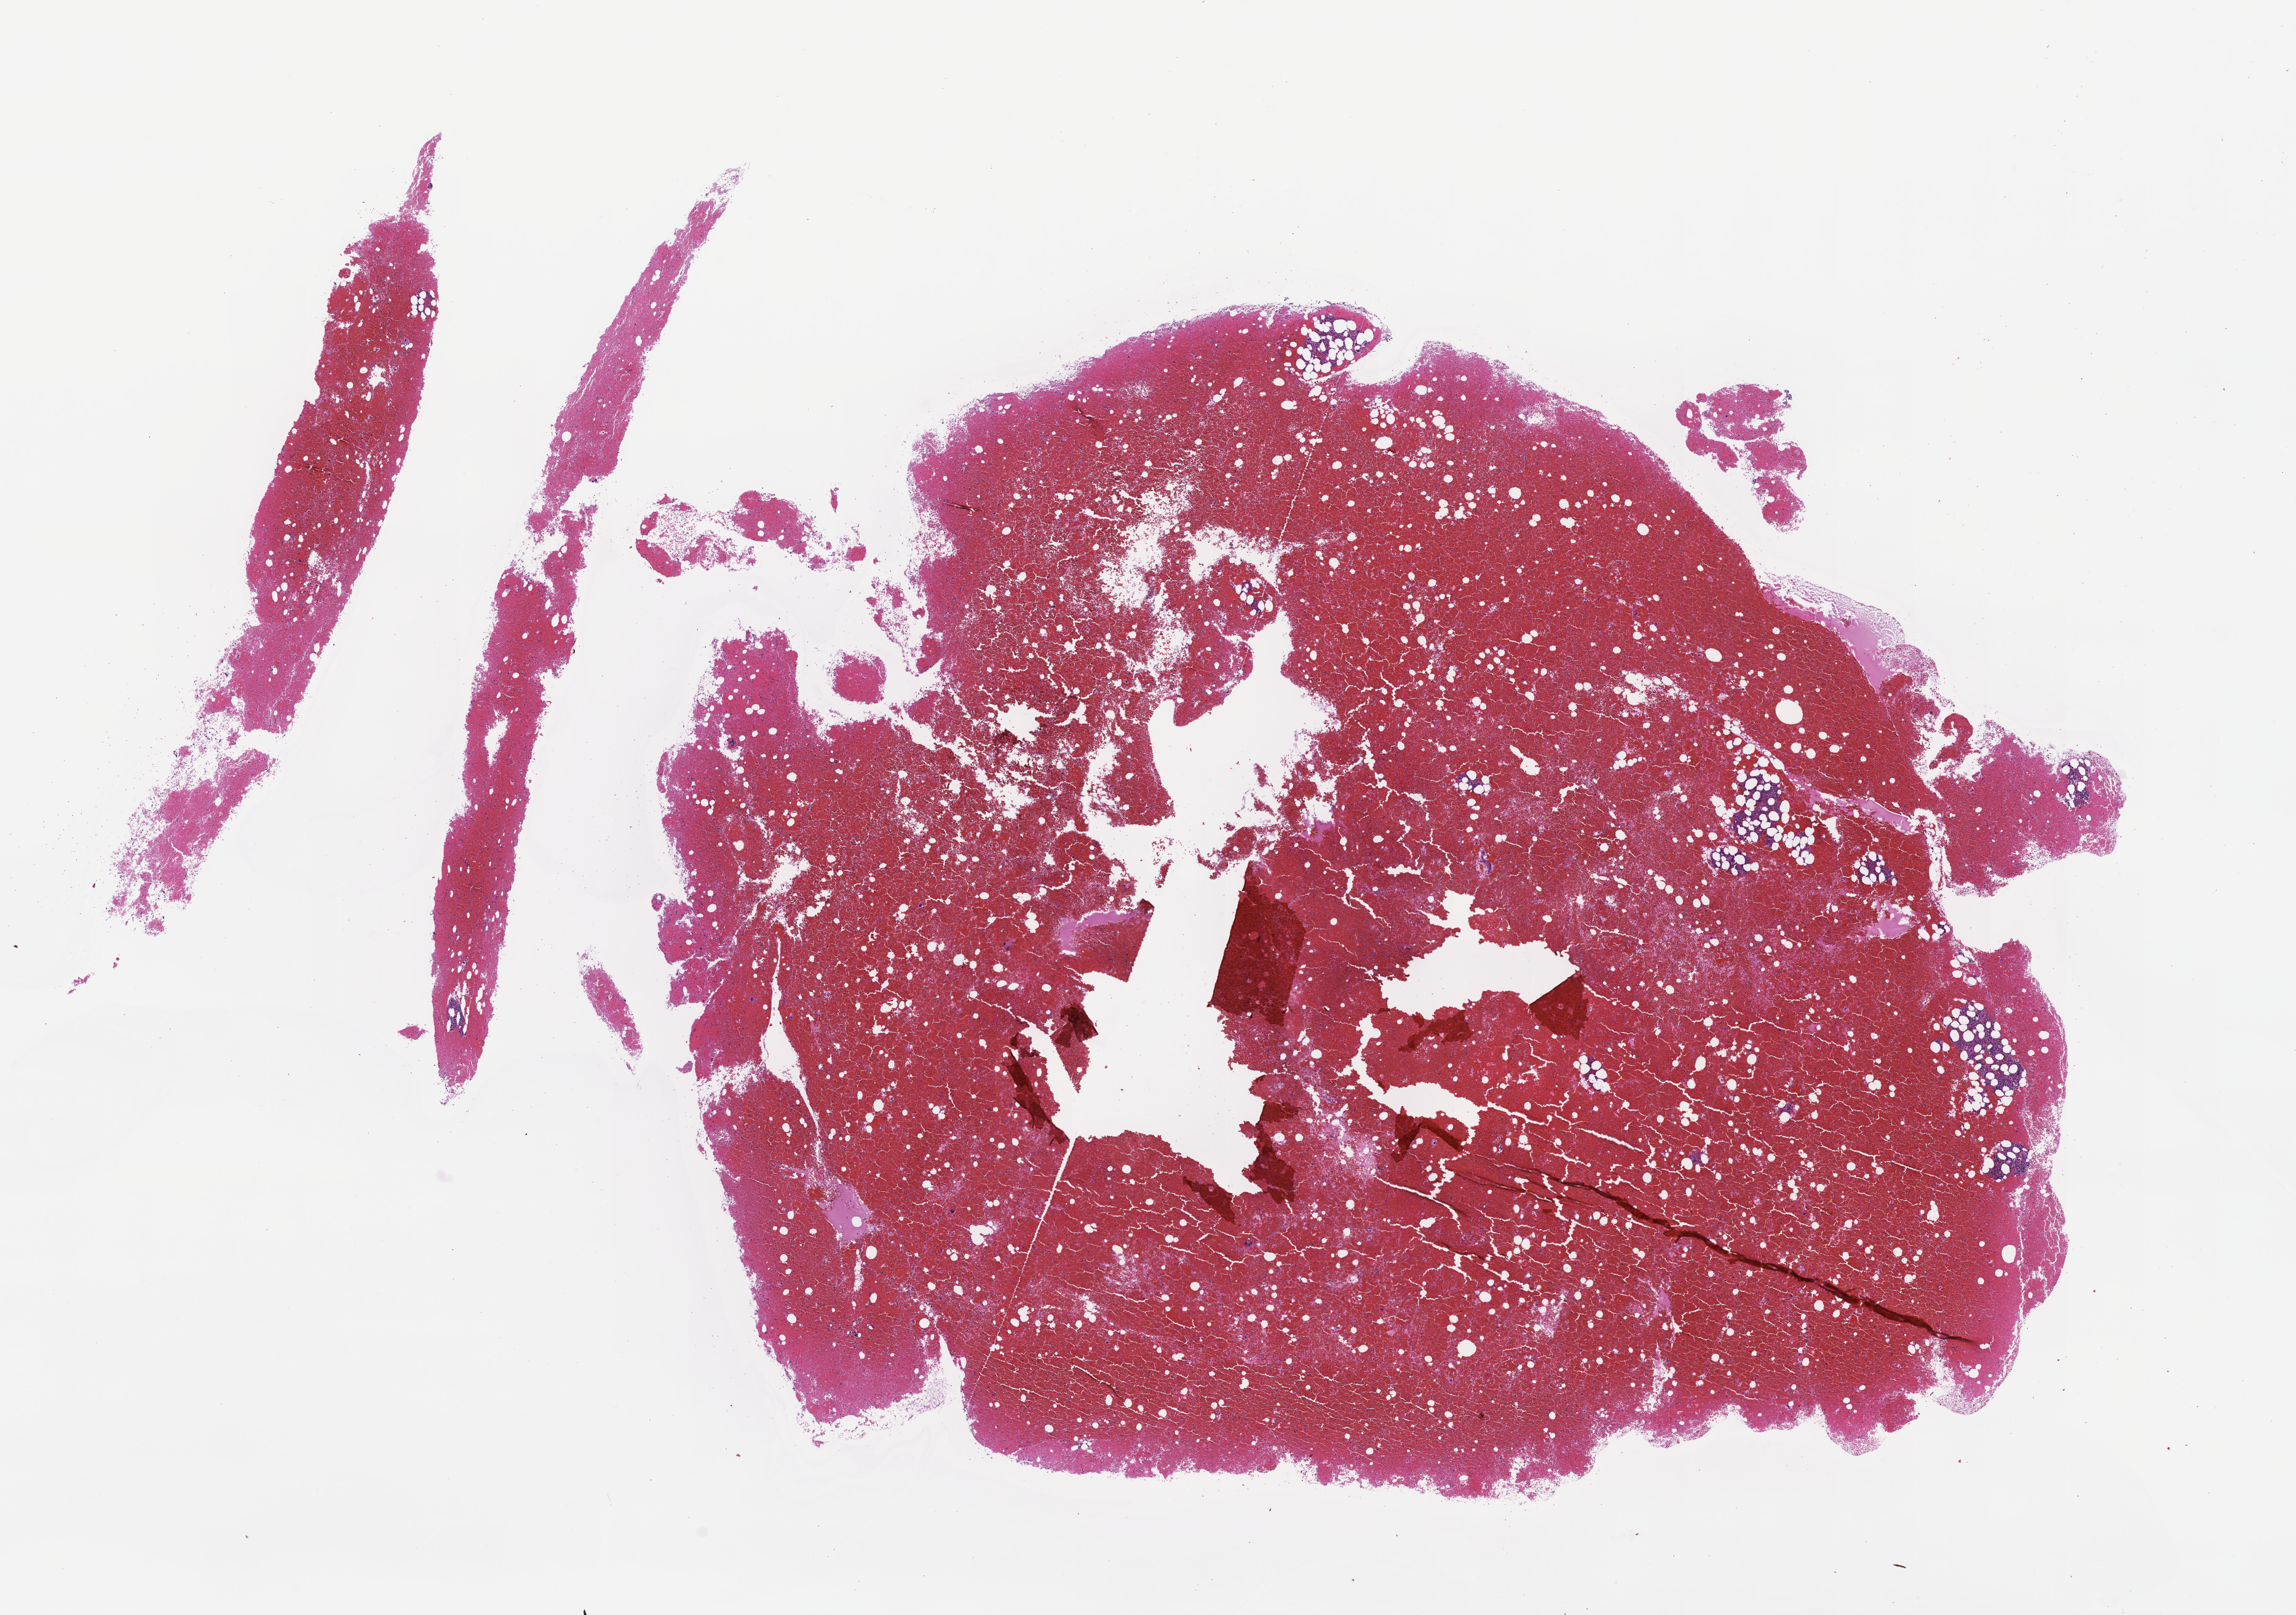
Whole-slide image, haematoxylin and eosin stain, low-resolution overview of the scanned area, about 15.1 x 10.6 mm; formalin-fixed, paraffin-embedded (FFPE) tissue; site: bone marrow; specimen time point: archival tissue. Patient sex: female.
This section: primary tumour tissue. Diagnosis: Plasma Cell Myeloma.